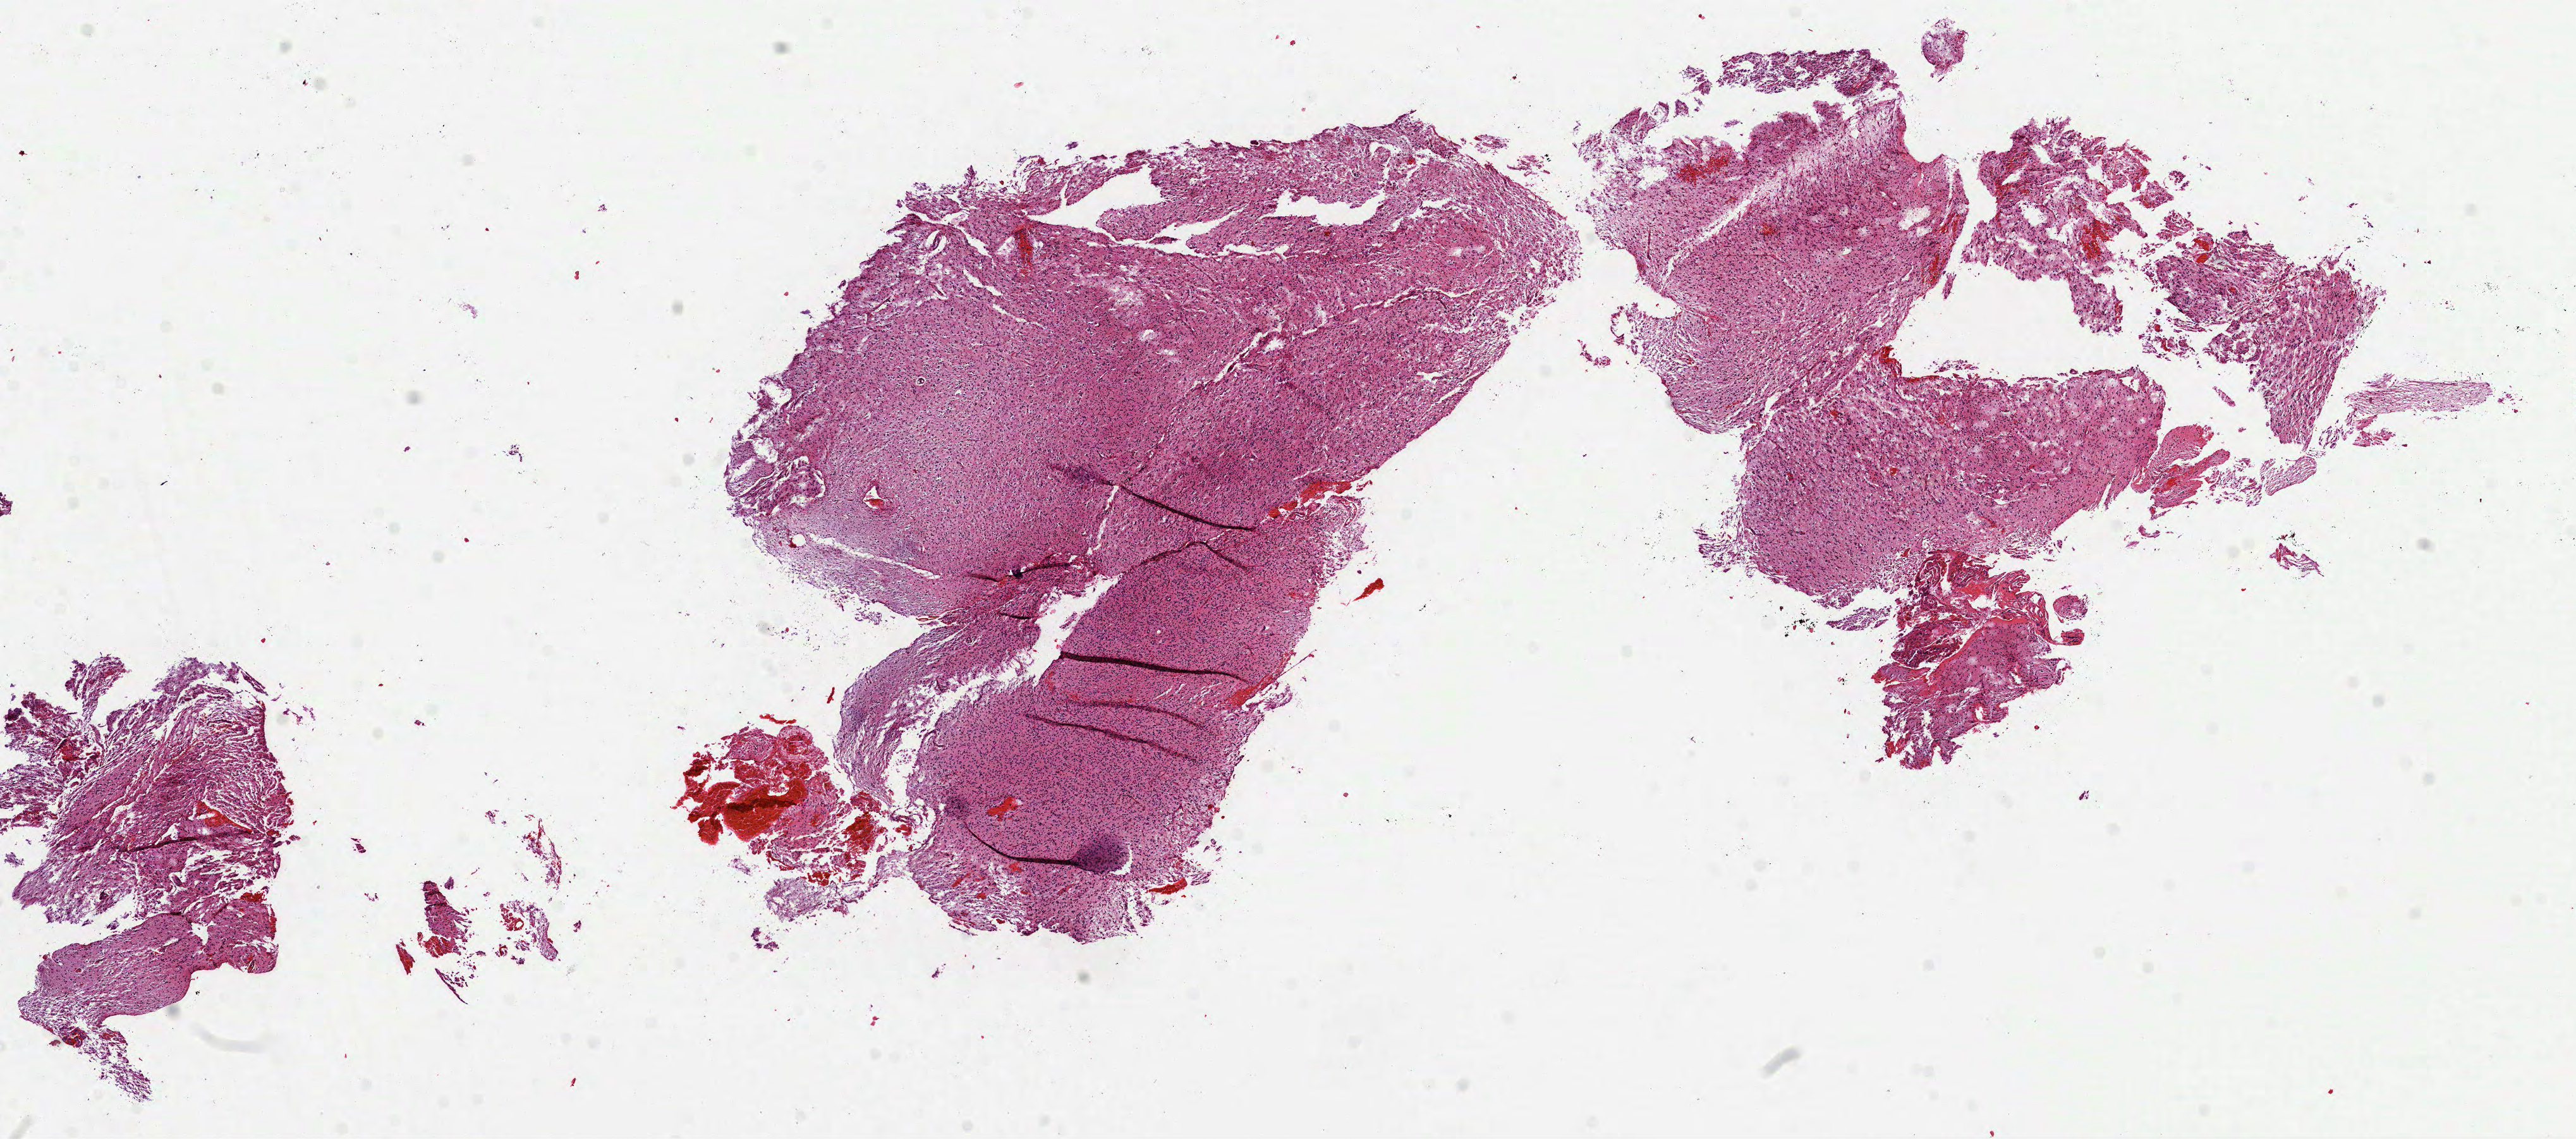
H&E-stained whole-slide image — whole scanned area (about 16.4 x 7.3 mm, from a 40x scan) shown as a low-resolution overview; formalin-fixed paraffin-embedded (FFPE) diagnostic section; brain, primary tumour sample. Male patient; age at initial diagnosis 31 years. Histologic grade: G3 (poorly differentiated).
Laterality: left. Histologic diagnosis: Astrocytoma, anaplastic.